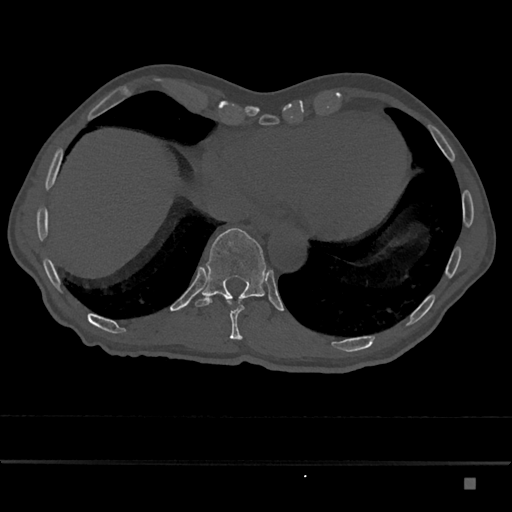
CT including the spine, one axial slice; slice 705 of 797 in the series (ordered by position); reconstruction kernel Br40s/3; bone window (W 1800 / L 400 HU); 0.5 mm slice thickness; 512 × 512 image matrix. Male patient, age 72 years. Case-level facts recorded for this patient, not image findings: primary cancer: prostate.
Structures marked on this image (semi-automatic segmentation, software-assisted and operator-edited):
- T10 vertebra: bounding box (x1, y1, x2, y2) in pixels: (226, 298, 244, 340)
- T11 vertebra: (195, 228, 267, 307)